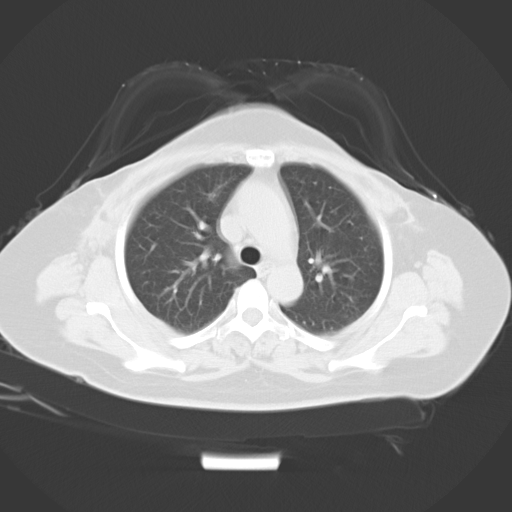
Chest CT, one axial slice; slice 17 of 25 in the series (ordered by position); reconstruction kernel B40f; lung window (W 1500 / L -600 HU); 10 mm slice thickness; 512 × 512 image matrix, field of view 410 × 410 mm. Female patient, age 55 years. From the clinical record (not read from this slice): clinical TNM (as recorded): T2 N0 M0.
Structures marked on this image (bounding box drawn by a radiologist):
- lung tumour (recorded histology: adenocarcinoma): bounding box [x1, y1, x2, y2] px = [198, 180, 229, 211]